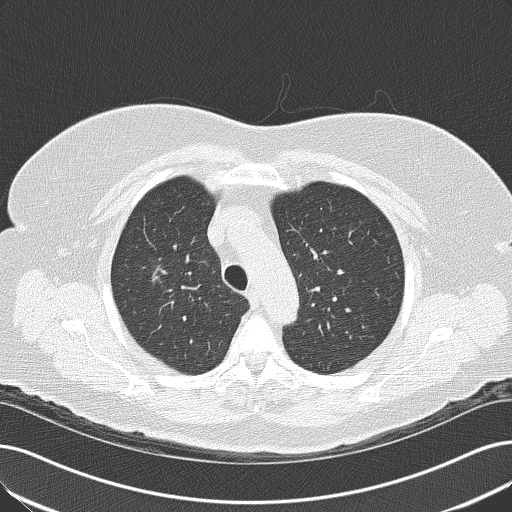
Low-dose screening chest CT, axial slice. First (baseline) screen. Lung window (W 1500 / L -600 HU). 2 mm slice thickness. 120 kVp. Female participant, aged 74 years at enrolment. Former smoker at enrolment.
Expert-annotated lung lesion, bounding box [x1, y1, x2, y2] px = [134, 247, 193, 304]. The screening reader recorded 2 non-calcified nodules or masses ≥4 mm on this exam; which of them this box marks is not recorded.